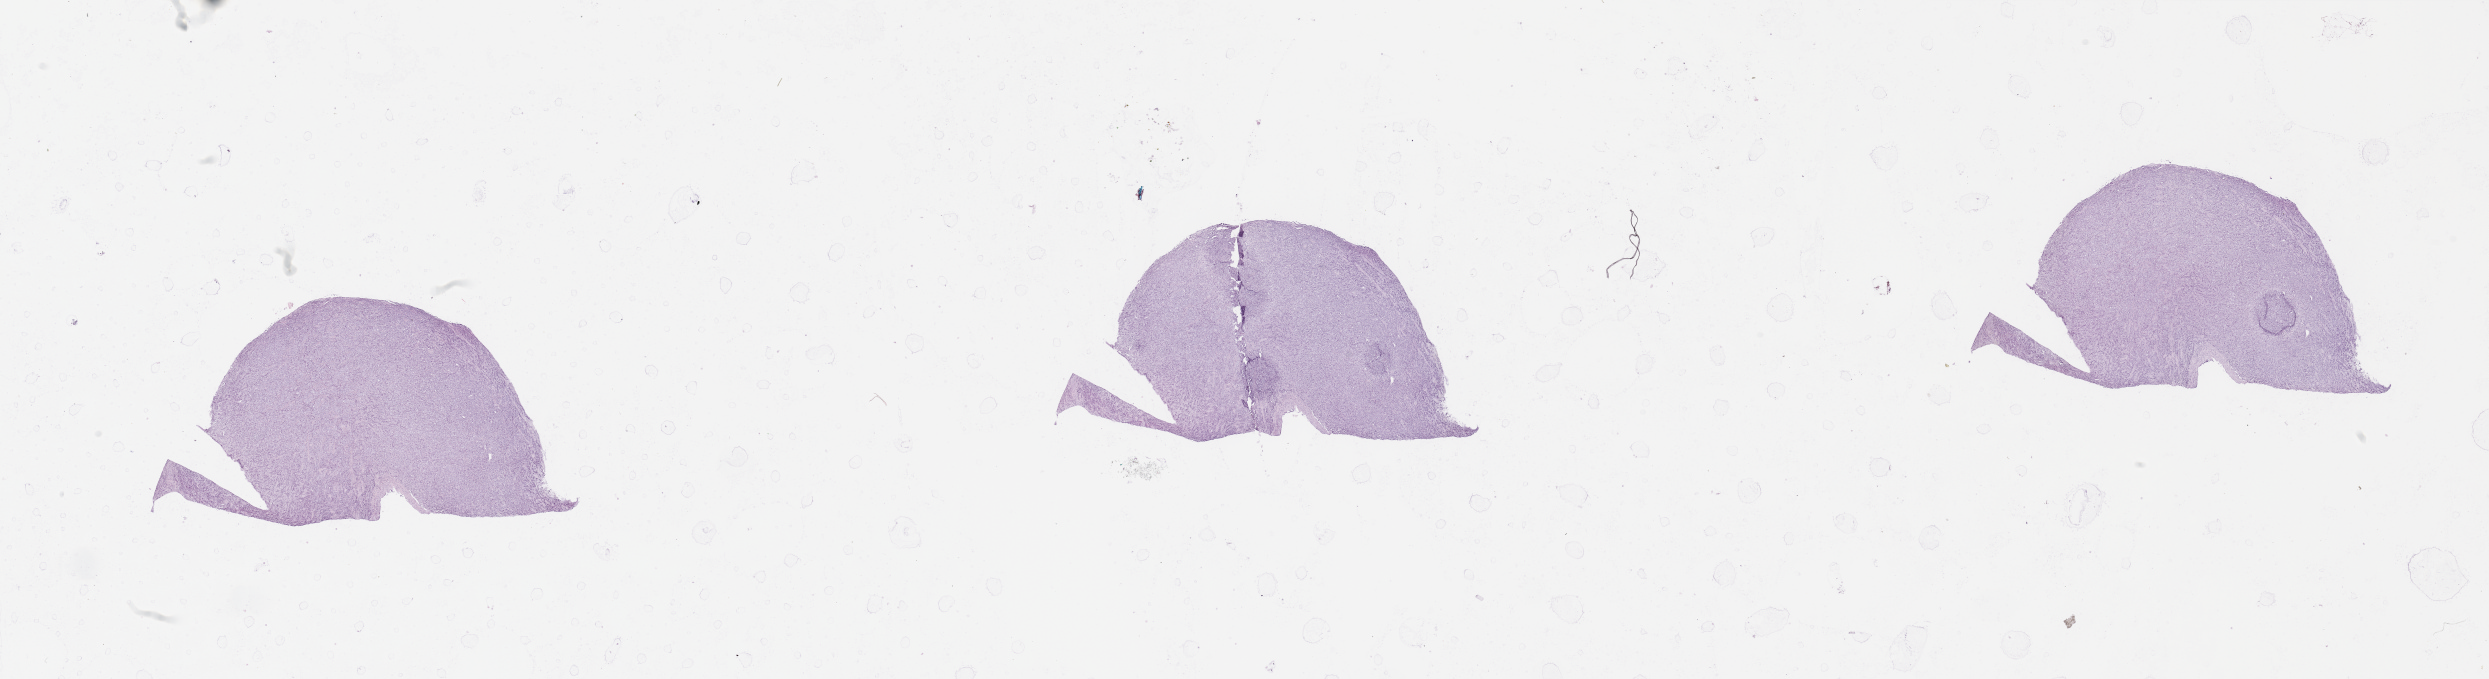
Whole-slide histology image, H&E — shown as a low-resolution overview of the whole scanned area (about 39.4 x 10.7 mm). Tumour tissue sample, sampled site: lung. Patient: male, age 51 years. Histologic grade: G2 (moderately differentiated). Composition of this section per pathologist review: tumour nuclei 80%, necrosis 0%.
Primary tumour site (as recorded): right middle lobe. Histologic diagnosis: Squamous cell carcinoma, NOS. AJCC pathologic stage: IIB.